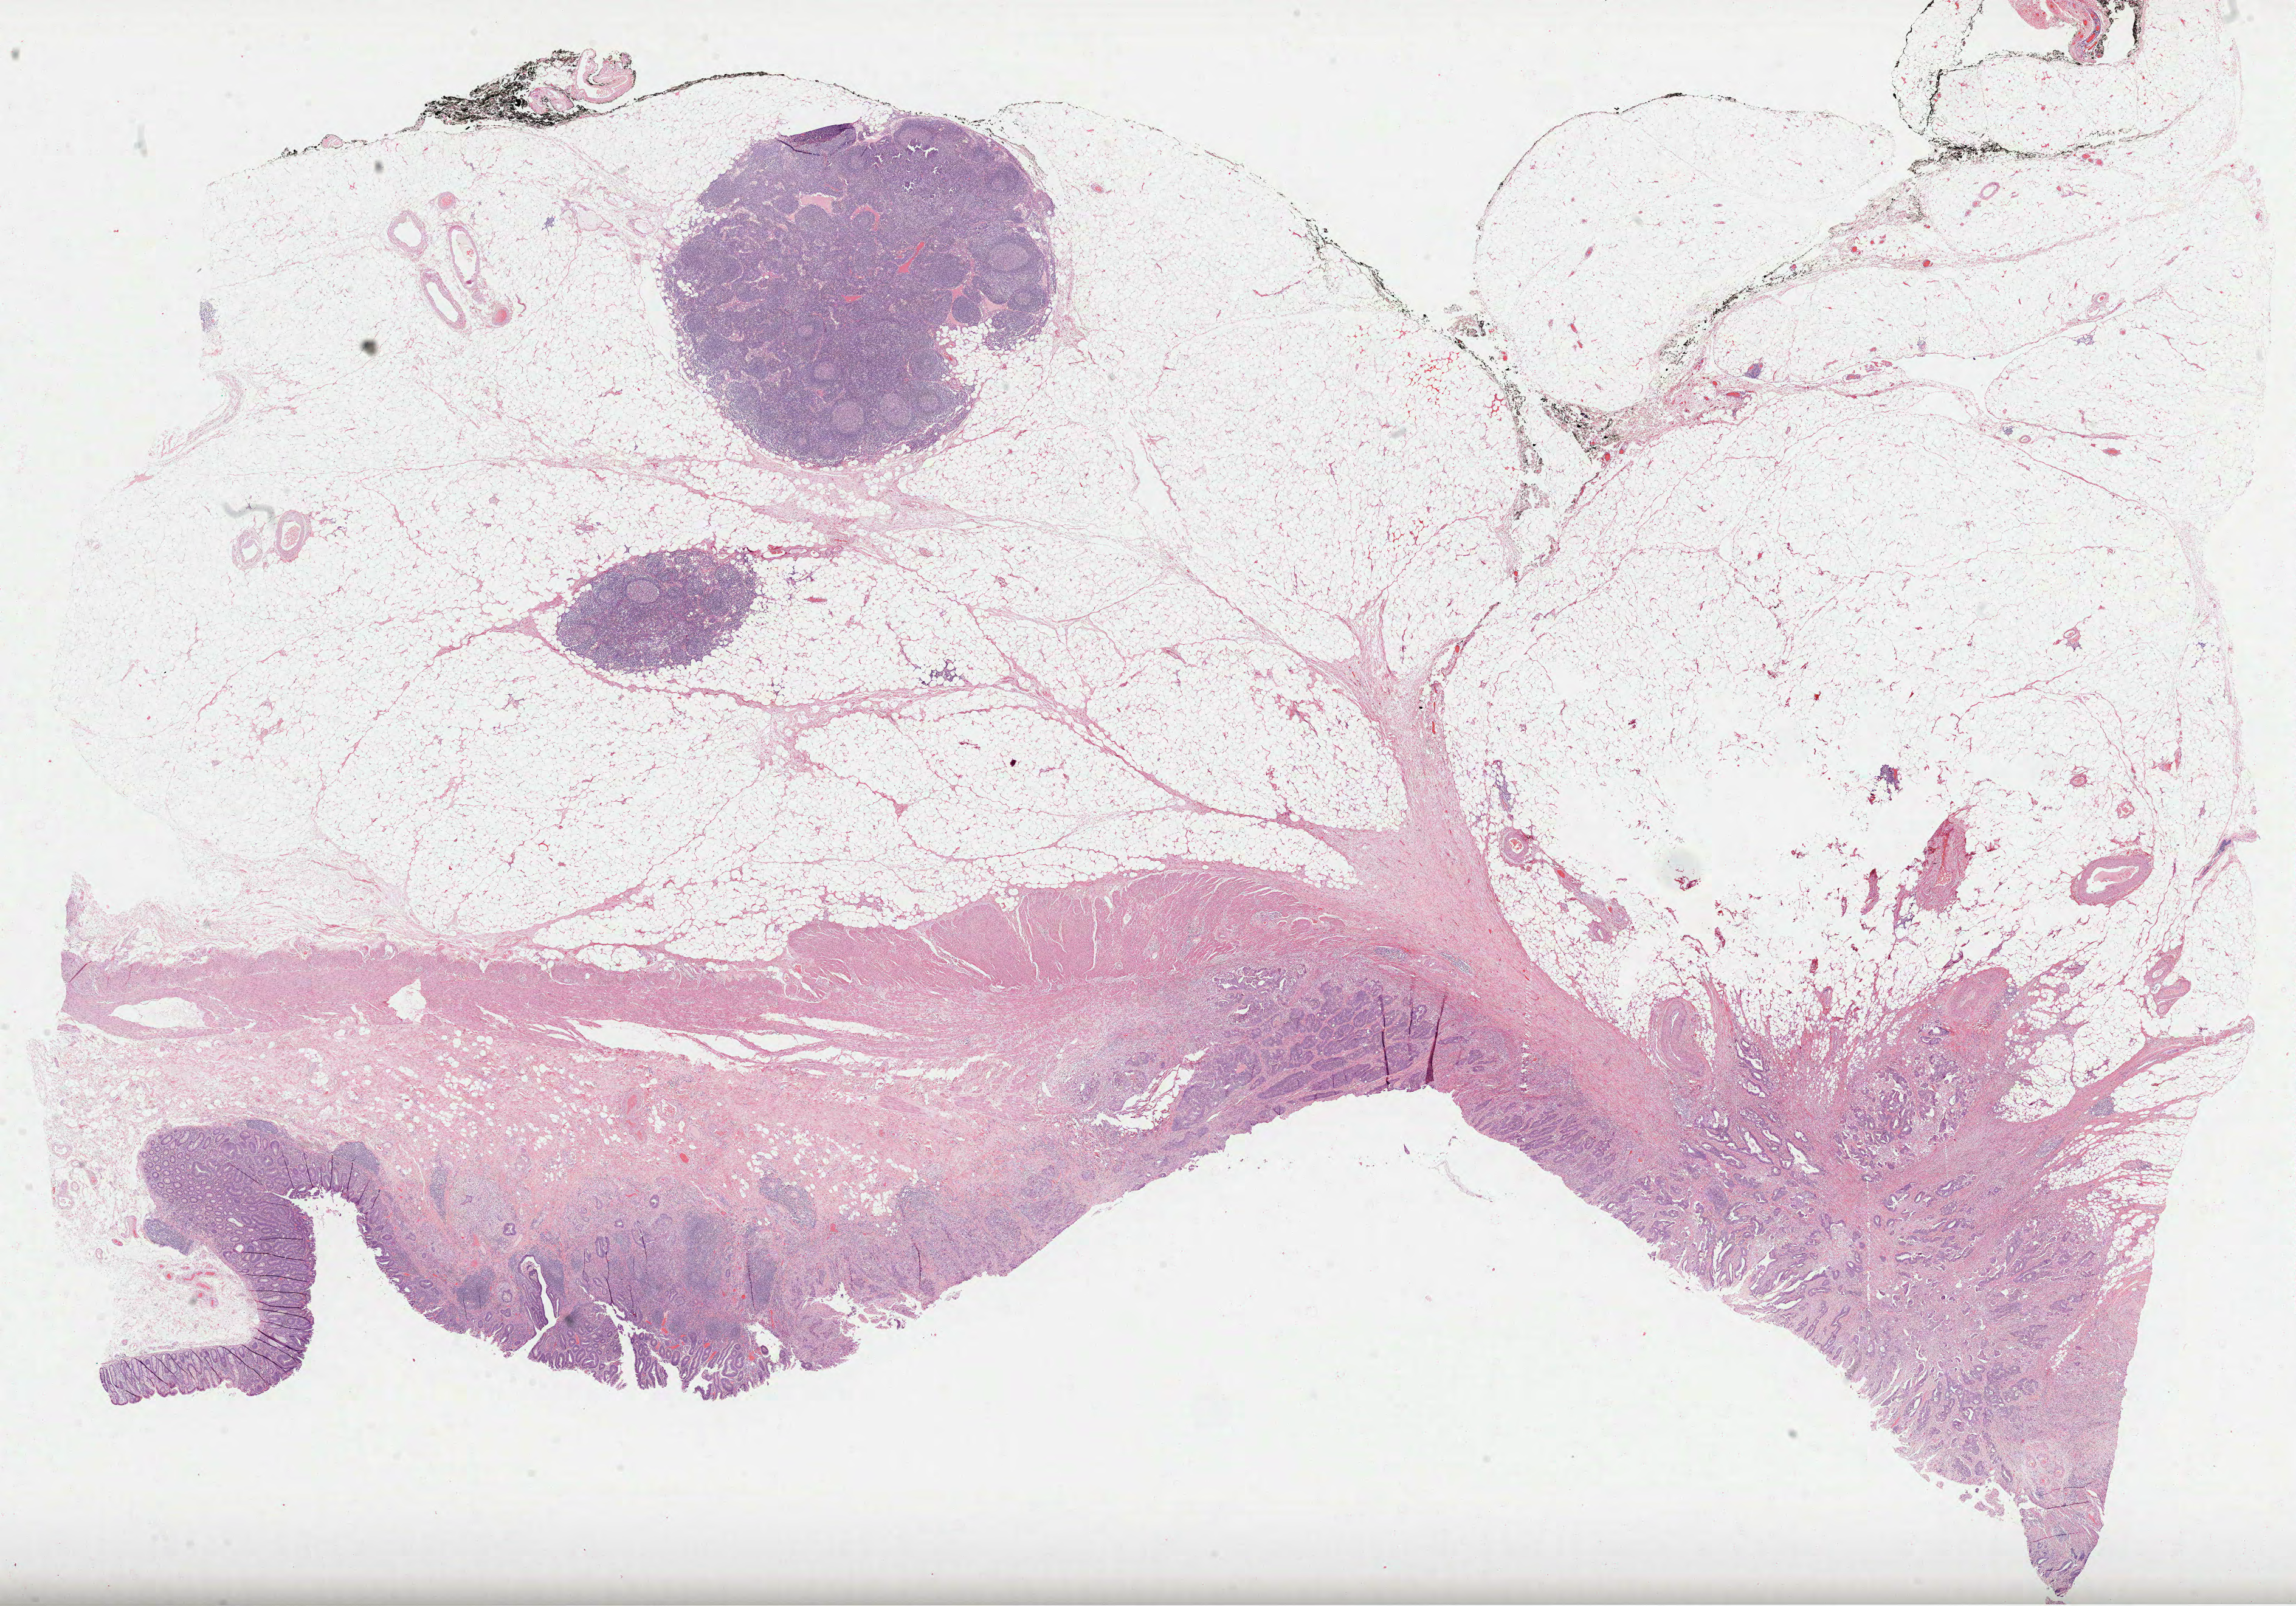
Whole-slide histology image, Hematoxylin and eosin (H&E) stained — a low-resolution overview of the entire scanned area, about 30.5 x 21.3 mm. Formalin-fixed paraffin-embedded (FFPE) diagnostic section. Primary tumour sample from the colon. Male patient; age at initial diagnosis 80 years.
AJCC pathologic stage: III (6th edition). Lymph nodes positive (case pathology): 1 of 37 examined. Diagnosis: Adenocarcinoma, NOS.